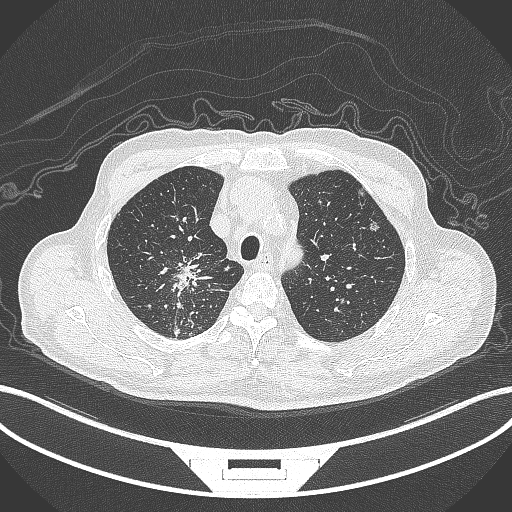
Chest CT, one axial slice. Slice 299 of 407 in the series (ordered by position). Reconstruction kernel B70f. Lung window (W 1500 / L -600 HU). 512 × 512 image matrix, field of view 400 × 400 mm. Male patient, age 69 years. Case-level facts recorded for this patient, not image findings: clinical TNM (as recorded): T1c N1 M1.
Annotated regions visible in this slice (bounding box drawn by a radiologist):
- lung tumour (recorded histology: adenocarcinoma): bounding box (x1, y1, x2, y2) in pixels: (169, 248, 215, 307)